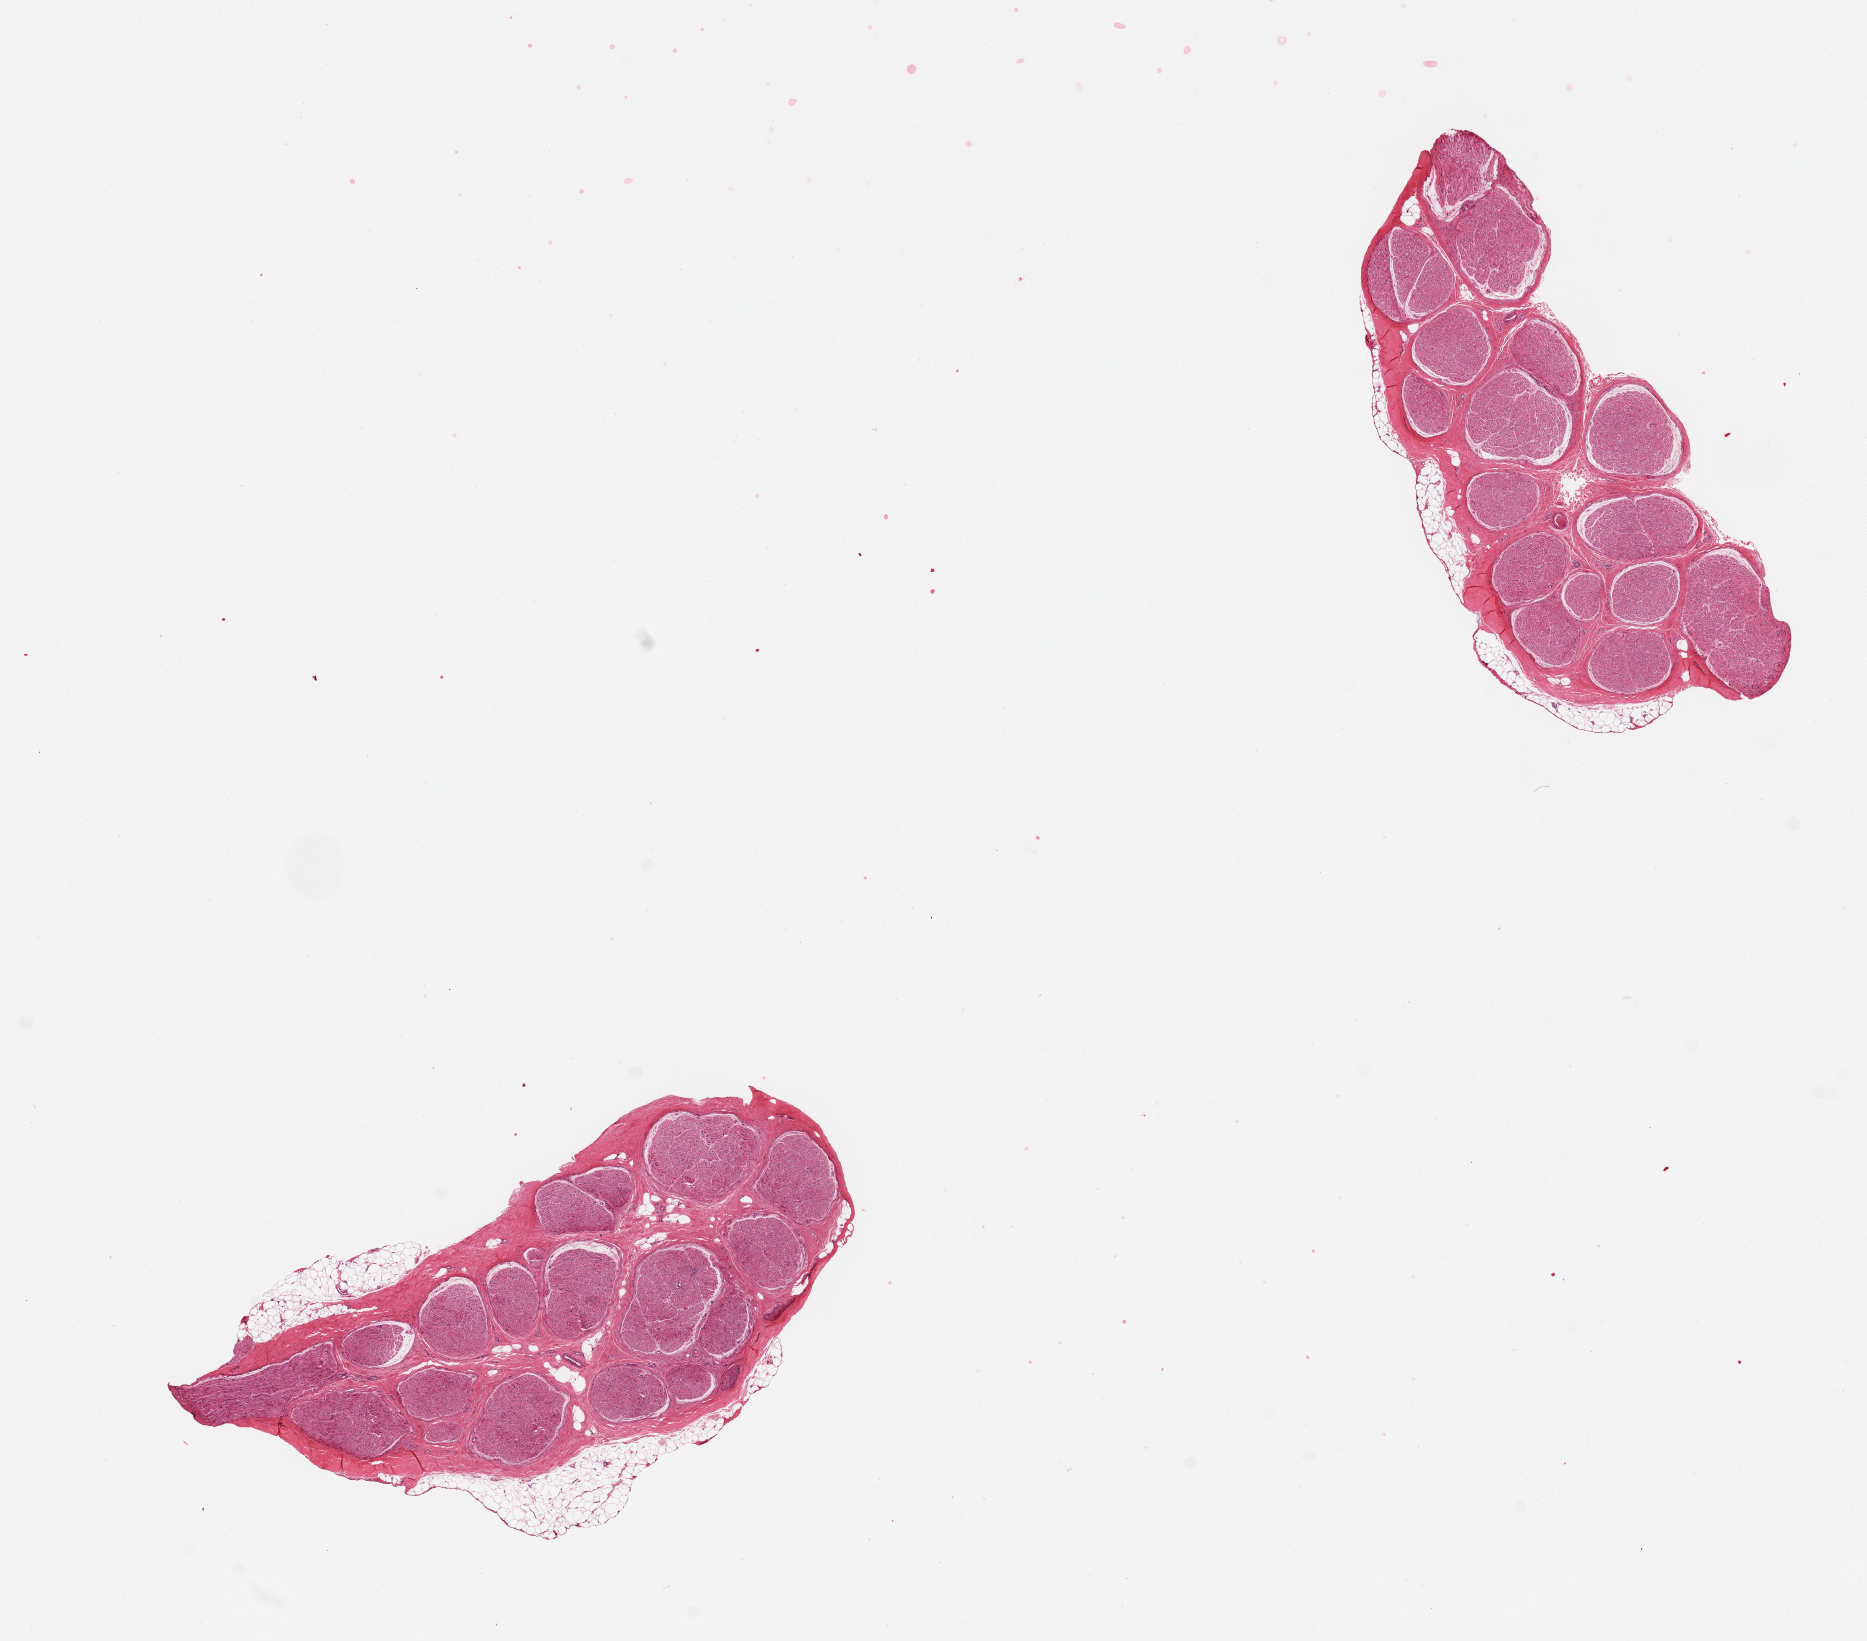
Digitized hematoxylin and eosin (H&E)-stained section, whole scanned area (about 14.8 x 13.0 mm, from a 20x scan) shown as a low-resolution overview, PAXgene-fixed paraffin-embedded (PFPE) section, section of tibial nerve (target tissue), tissue donor sample. Male donor.
- reviewer comment on this tissue sample: 2 pieces; 10% external fat, <5% internal fat